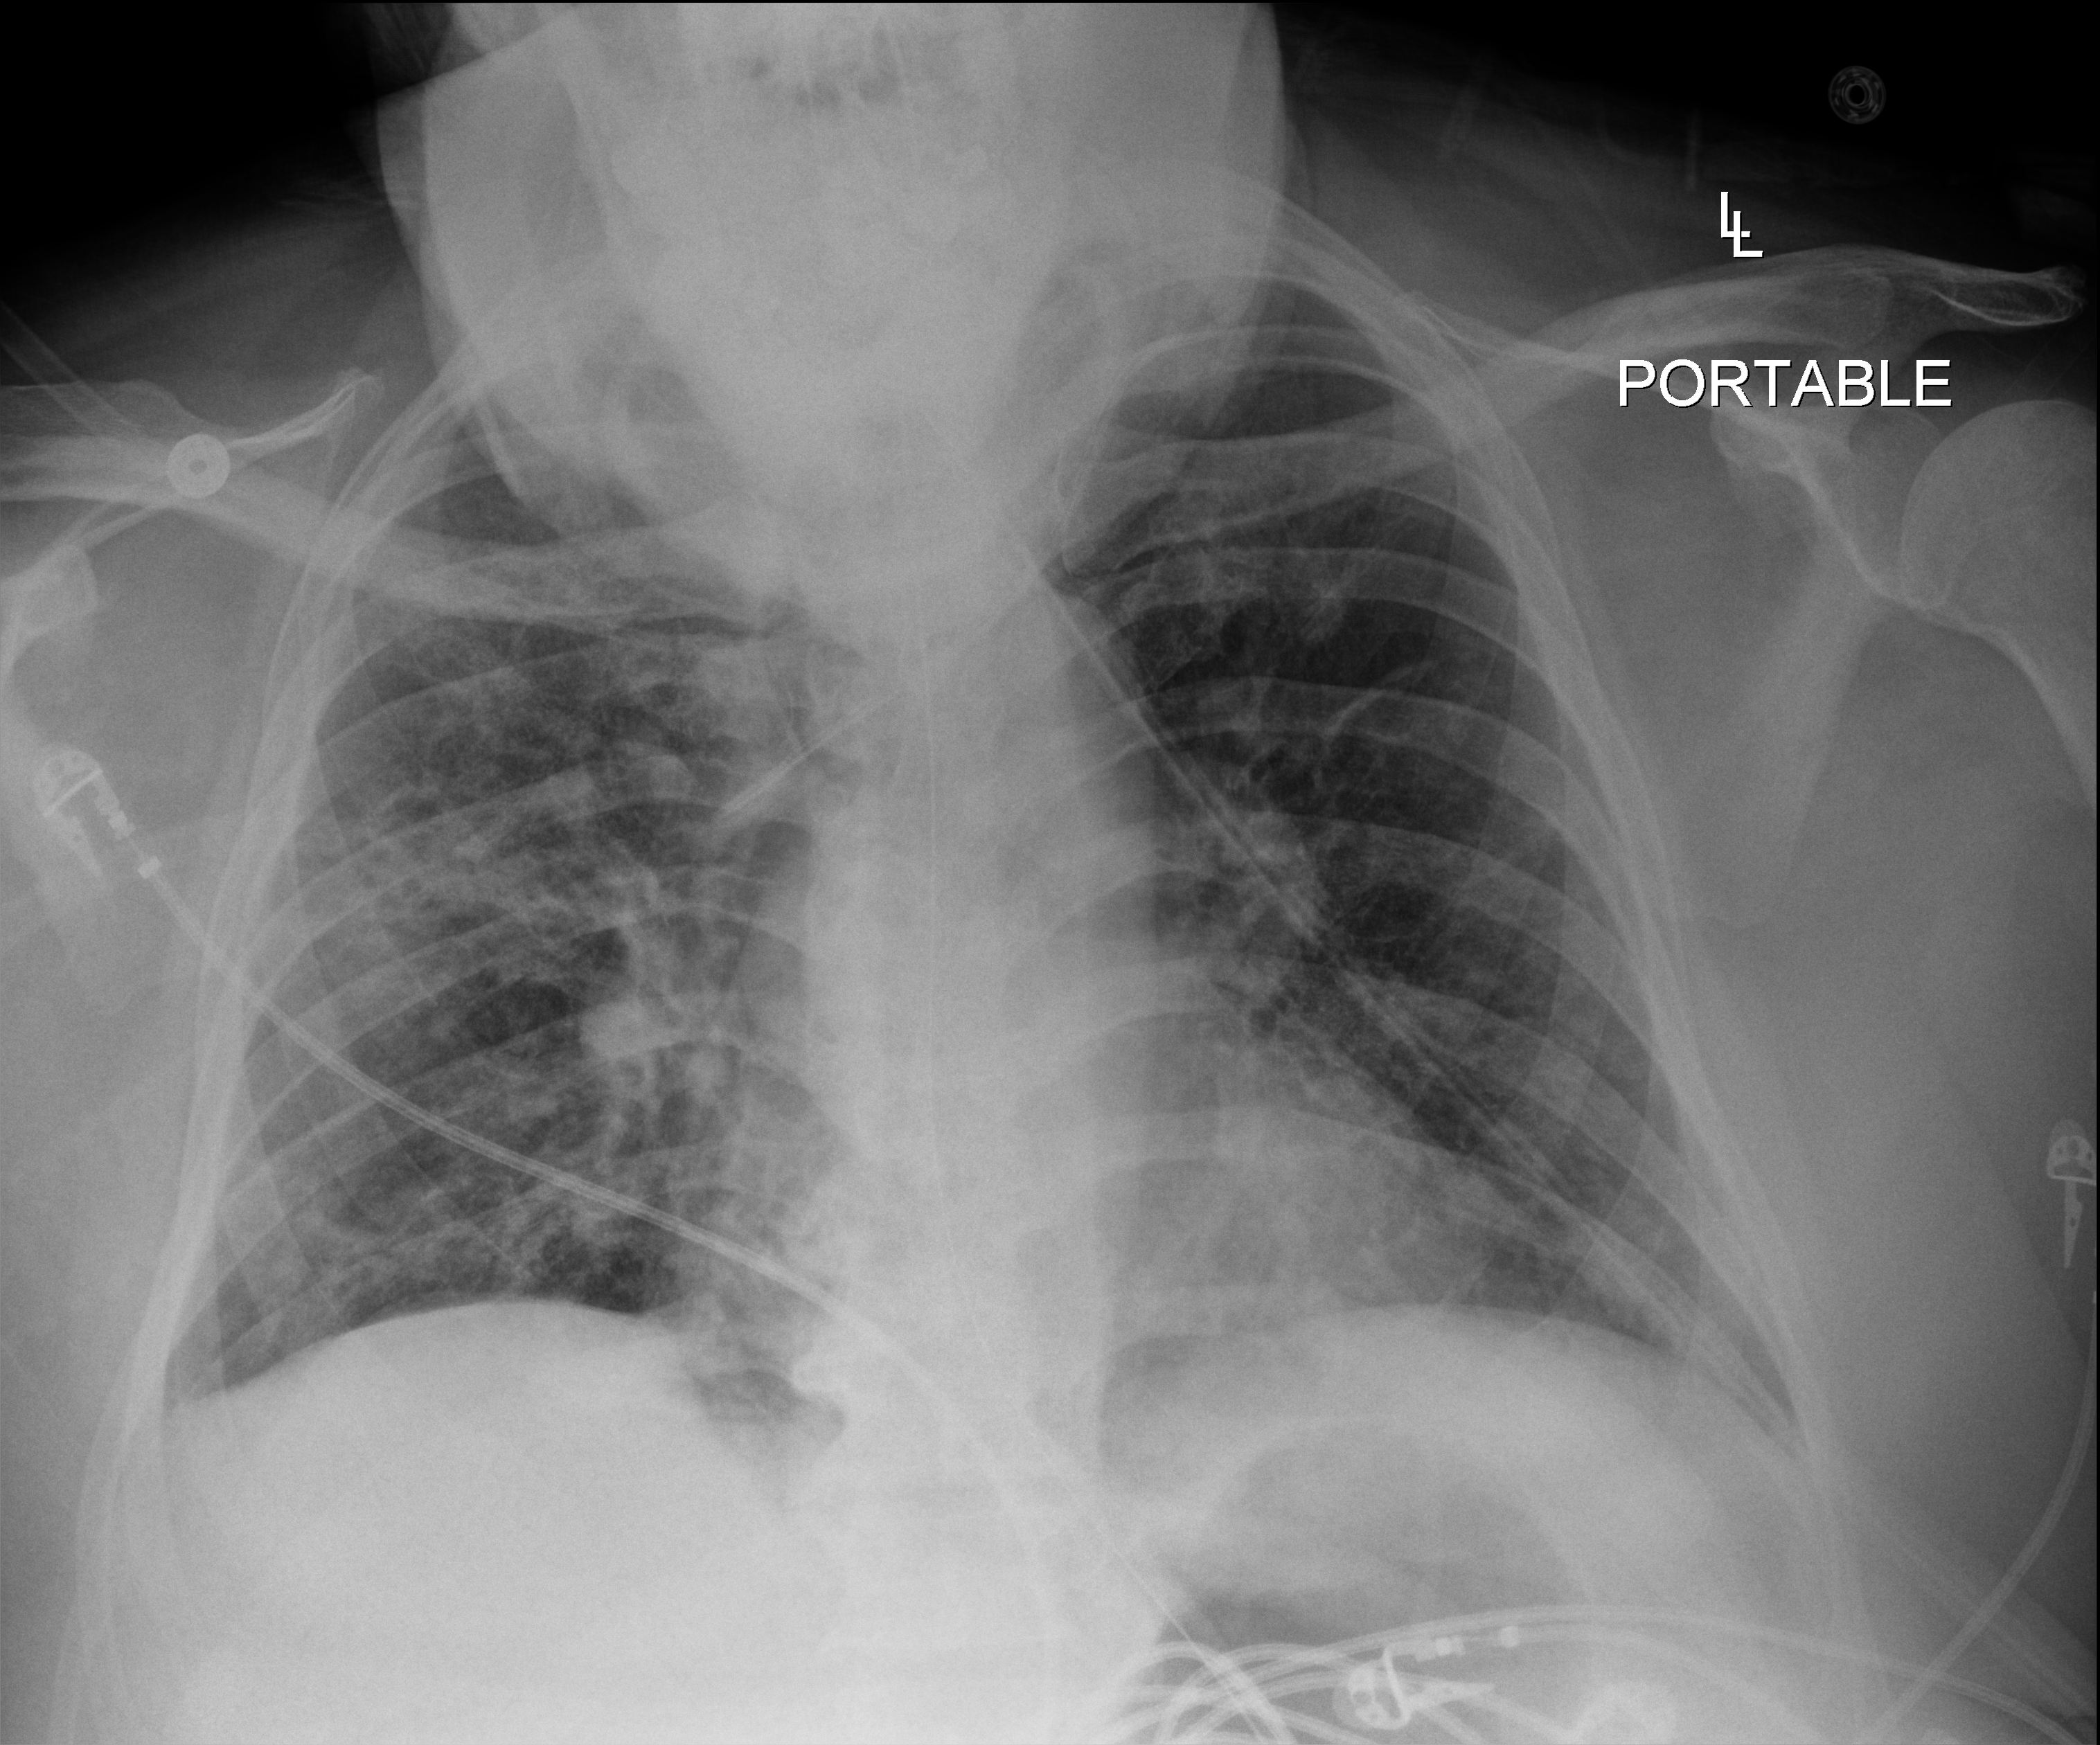
Chest radiograph; anteroposterior (AP) projection. Male patient hospitalised with COVID-19, age 18–59 years.
Hospital-stay facts (about this admission, not read from this image; timing relative to this image not recorded):
- chronic kidney disease (admission record): no
- admitted to intensive care during this hospital stay: yes